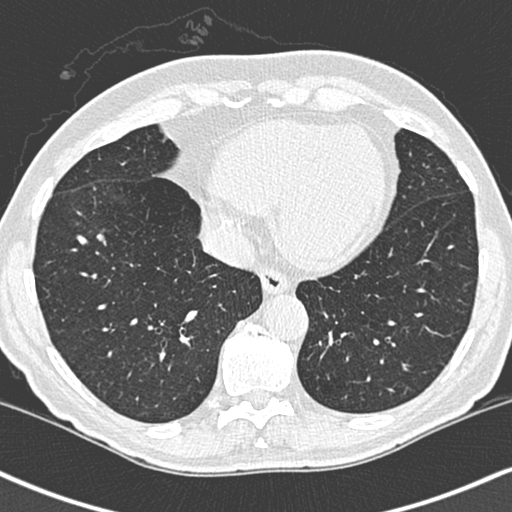
Low-dose screening chest CT, one axial slice. Position 86 of 248 along the scan axis. 120 kVp. Lung window (W 1500 / L -600 HU). 1.3 mm slice thickness. 512 × 512 image matrix, field of view 323 × 323 mm.
Annotated regions visible in this slice (manually delineated by an expert):
- lesion 1 (tumor, lower lobe of right lung): bounding box [x1, y1, x2, y2] px = [113, 226, 132, 230]